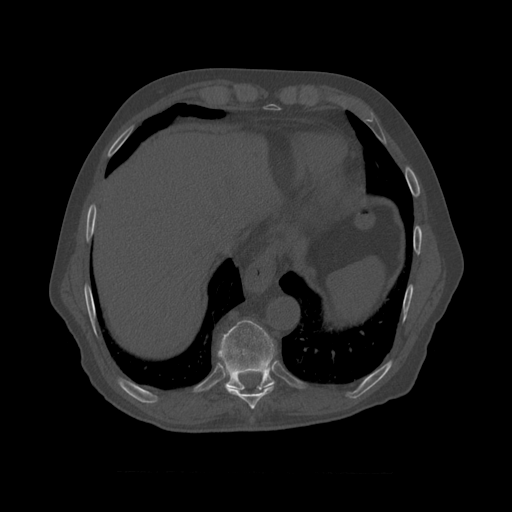
CT including the spine, one axial slice; position 436 of 450 along the scan axis; reconstruction kernel STANDARD; 120 kVp; bone window (W 1800 / L 400 HU); 512 × 512 image matrix, field of view 405 × 405 mm. Patient age 75 years. Case-level facts recorded for this patient, not image findings: primary cancer: prostate.
Structures marked on this image (semi-automatically segmented with operator editing):
- T8 vertebra: bounding box <219,340,275,410> (left, top, right, bottom; pixels)
- T9 vertebra: <218,320,275,390>